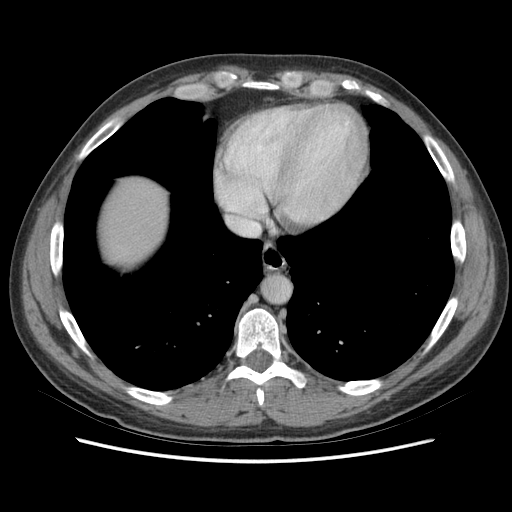
Contrast-enhanced abdominal CT (liver protocol), one axial slice; position 69 of 73 along the scan axis; soft-tissue window (W 400 / L 40 HU); 2.5 mm slice thickness; 512 × 512 image matrix. Case-level facts recorded for this patient, not image findings: diagnosis: hepatocellular carcinoma (patient treated with transarterial chemoembolisation; whether this scan precedes or follows treatment is not stated here); TNM stage (as recorded): Stage-IIIA; Child-Pugh class: A; tumour size: 6.6 cm.
Outlined on this slice (semi-automatic segmentation, software-assisted and operator-edited):
- abdominal aorta: bounding box (x1, y1, x2, y2) in pixels: (263, 277, 290, 303)
- liver parenchyma outside the tumour (the mass and vessels are separate outlines, so this box may not span the whole liver): (100, 178, 166, 262)